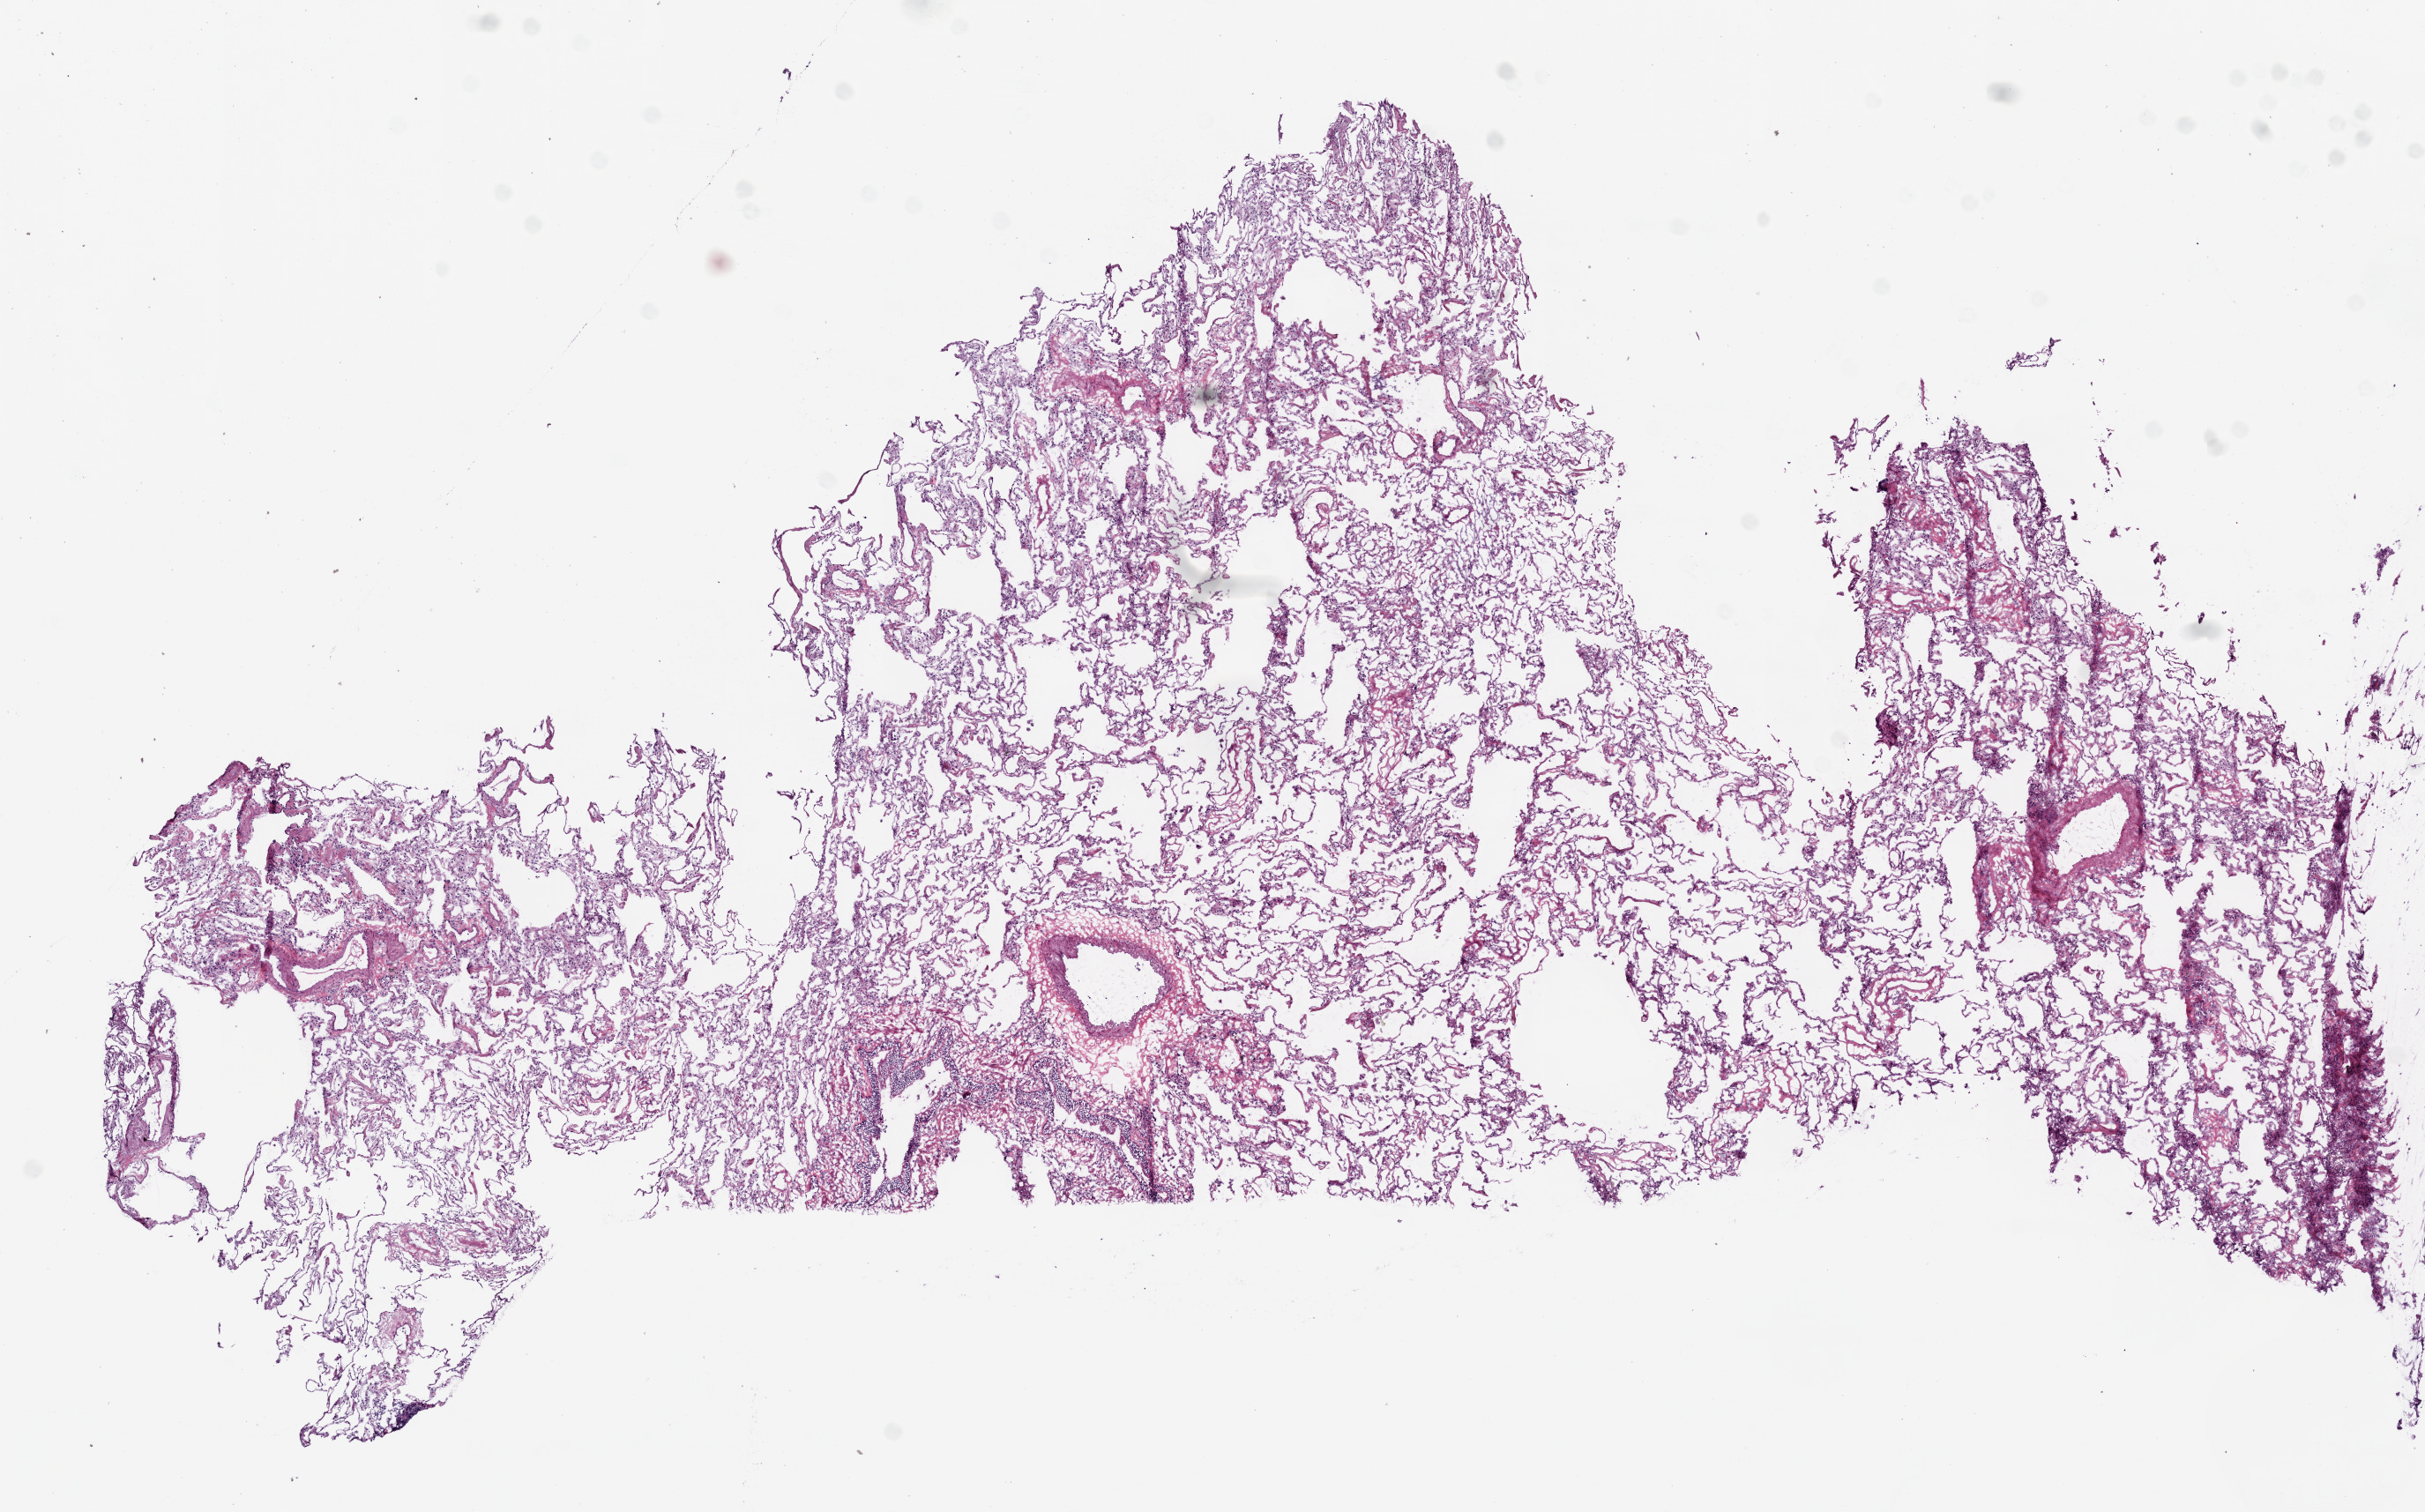
Whole-slide histology image, Hematoxylin and eosin (H&E) stained — whole scanned area (about 11.0 x 6.9 mm) shown as a low-resolution overview. Frozen section from the bottom of the tissue portion. Lung, solid tissue normal (non-tumour tissue) sample. Patient: female, age at initial diagnosis 73 years.
This section: solid tissue normal sample (biorepository sample class). Patient diagnosis: Squamous cell carcinoma, NOS (overlapping lesion of lung).